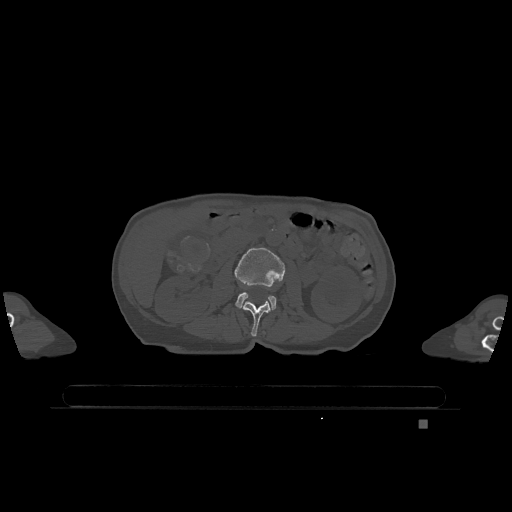
CT including the spine, one axial slice. Slice 388 of 1317 in the series (ordered by position). Bone window (W 1800 / L 400 HU). 0.5 mm slice thickness. 512 × 512 image matrix, field of view 500 × 500 mm. Female patient, age 74 years. Case-level facts recorded for this patient, not image findings: primary cancer: lung.
Outlined on this slice (semi-automatic segmentation, software-assisted and operator-edited):
- L2 vertebra: box from (x=243, y=301) to (x=271, y=337) px
- L3 vertebra: (x=234, y=248)–(x=285, y=310)